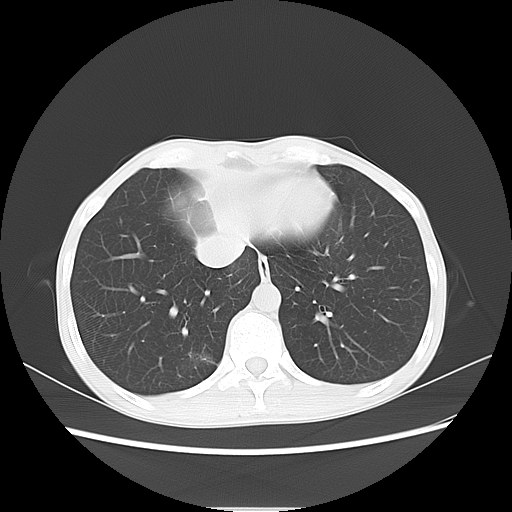
Chest CT, one axial slice. Position 21 of 69 along the scan axis. Reconstruction kernel LUNG. 120 kVp. Lung window (W 1500 / L -600 HU). 512 × 512 image matrix, field of view 350 × 350 mm. Patient: female, 51 years. From the clinical record (not read from this slice): clinical TNM (as recorded): T1c N0 M0; histopathological grade: G2-3.
Annotated regions visible in this slice (rectangle marked by the reading radiologist):
- lung tumour (recorded histology: adenocarcinoma): bounding box (x1, y1, x2, y2) in pixels: (183, 342, 223, 377)